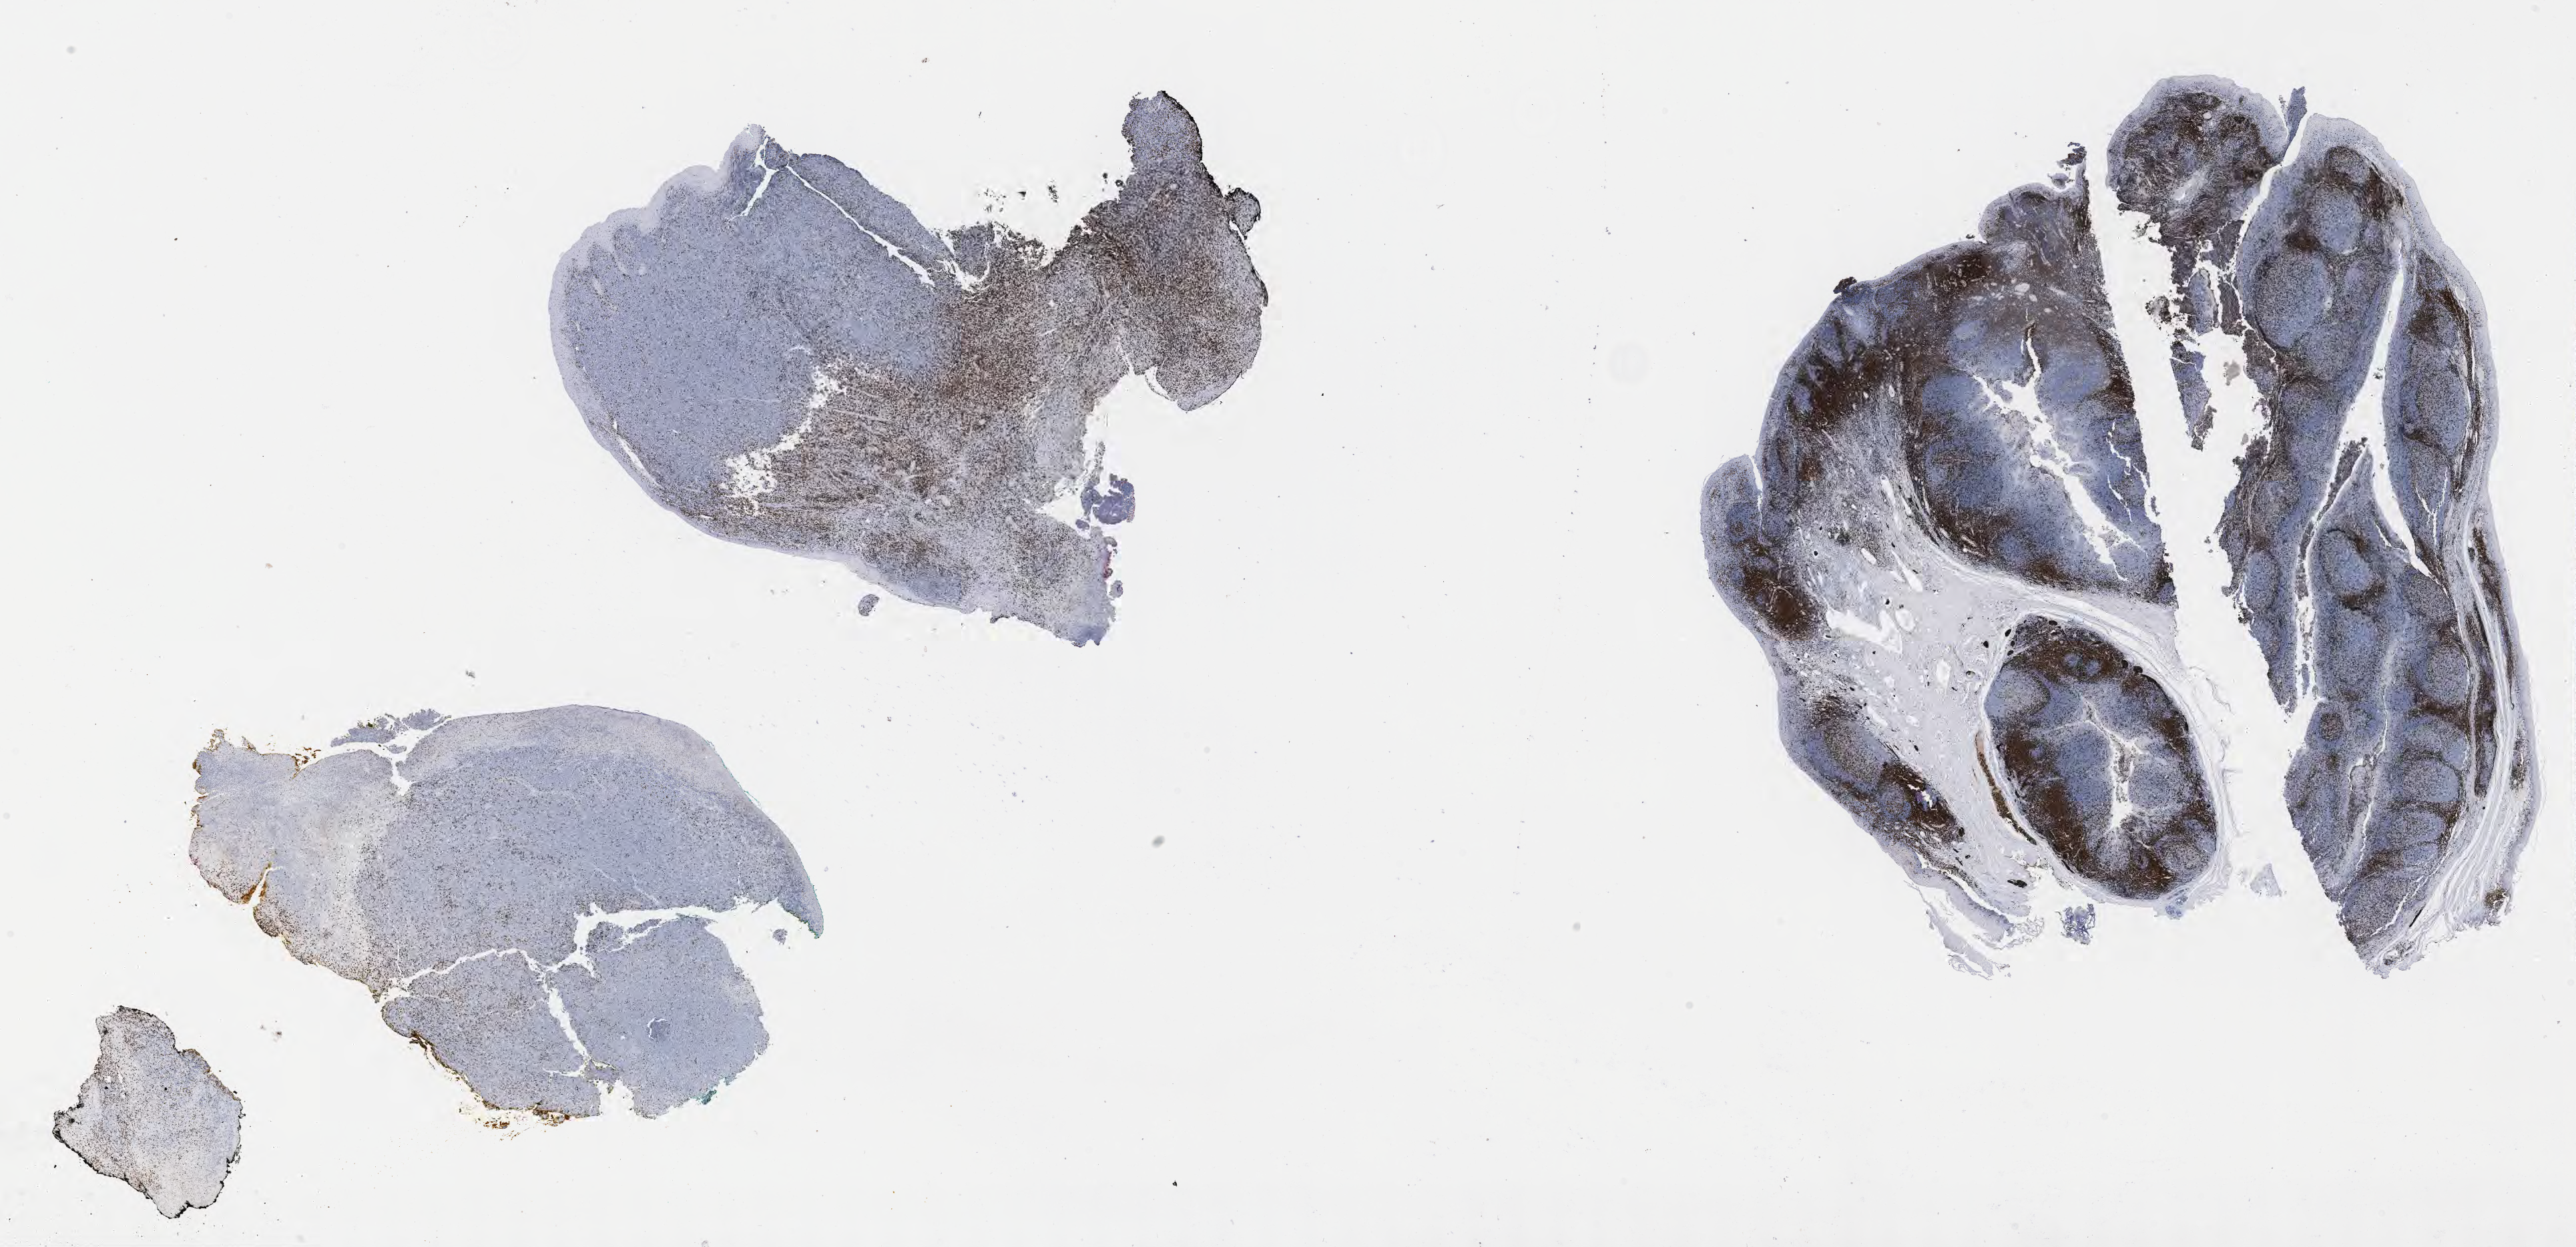
Immunohistochemistry (IHC) whole-slide image stained for CD3 — whole scanned area (about 31.2 x 15.1 mm) shown as a low-resolution overview. Specimen: tumor tissue. Patient: male, 49 years old.
• diagnosis: Diffuse large B-cell lymphoma, NOS